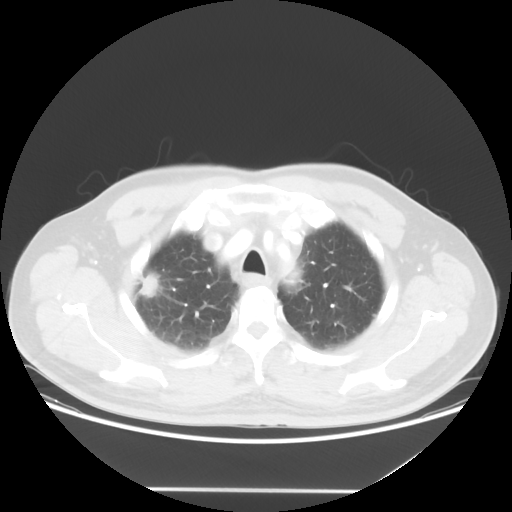
Chest CT, one axial slice. Slice 44 of 54 in the series (ordered by position). 120 kVp. Lung window (W 1500 / L -600 HU). 5 mm slice thickness. 512 × 512 image matrix, field of view 416 × 416 mm. Patient: male, 65 years. Case-level facts recorded for this patient, not image findings: clinical TNM (as recorded): T1c N1 M0.
Outlined on this slice (bounding box drawn by a radiologist):
- lung tumour (recorded histology: adenocarcinoma): bounding box <131,268,172,304> (left, top, right, bottom; pixels)